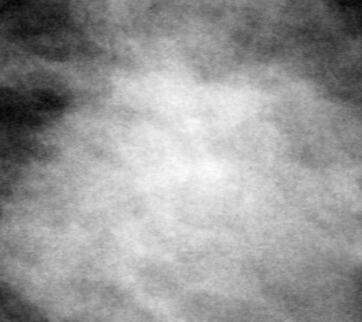
Region of interest cut from a scanned film mammogram (one marked finding); right breast; MLO view.
Finding: mass, shape irregular, margins ill defined; BI-RADS assessment category 4; subtlety rating 3 on a 1 (subtle) to 5 (obvious) scale; pathology result (as recorded, not read from the image): malignant.